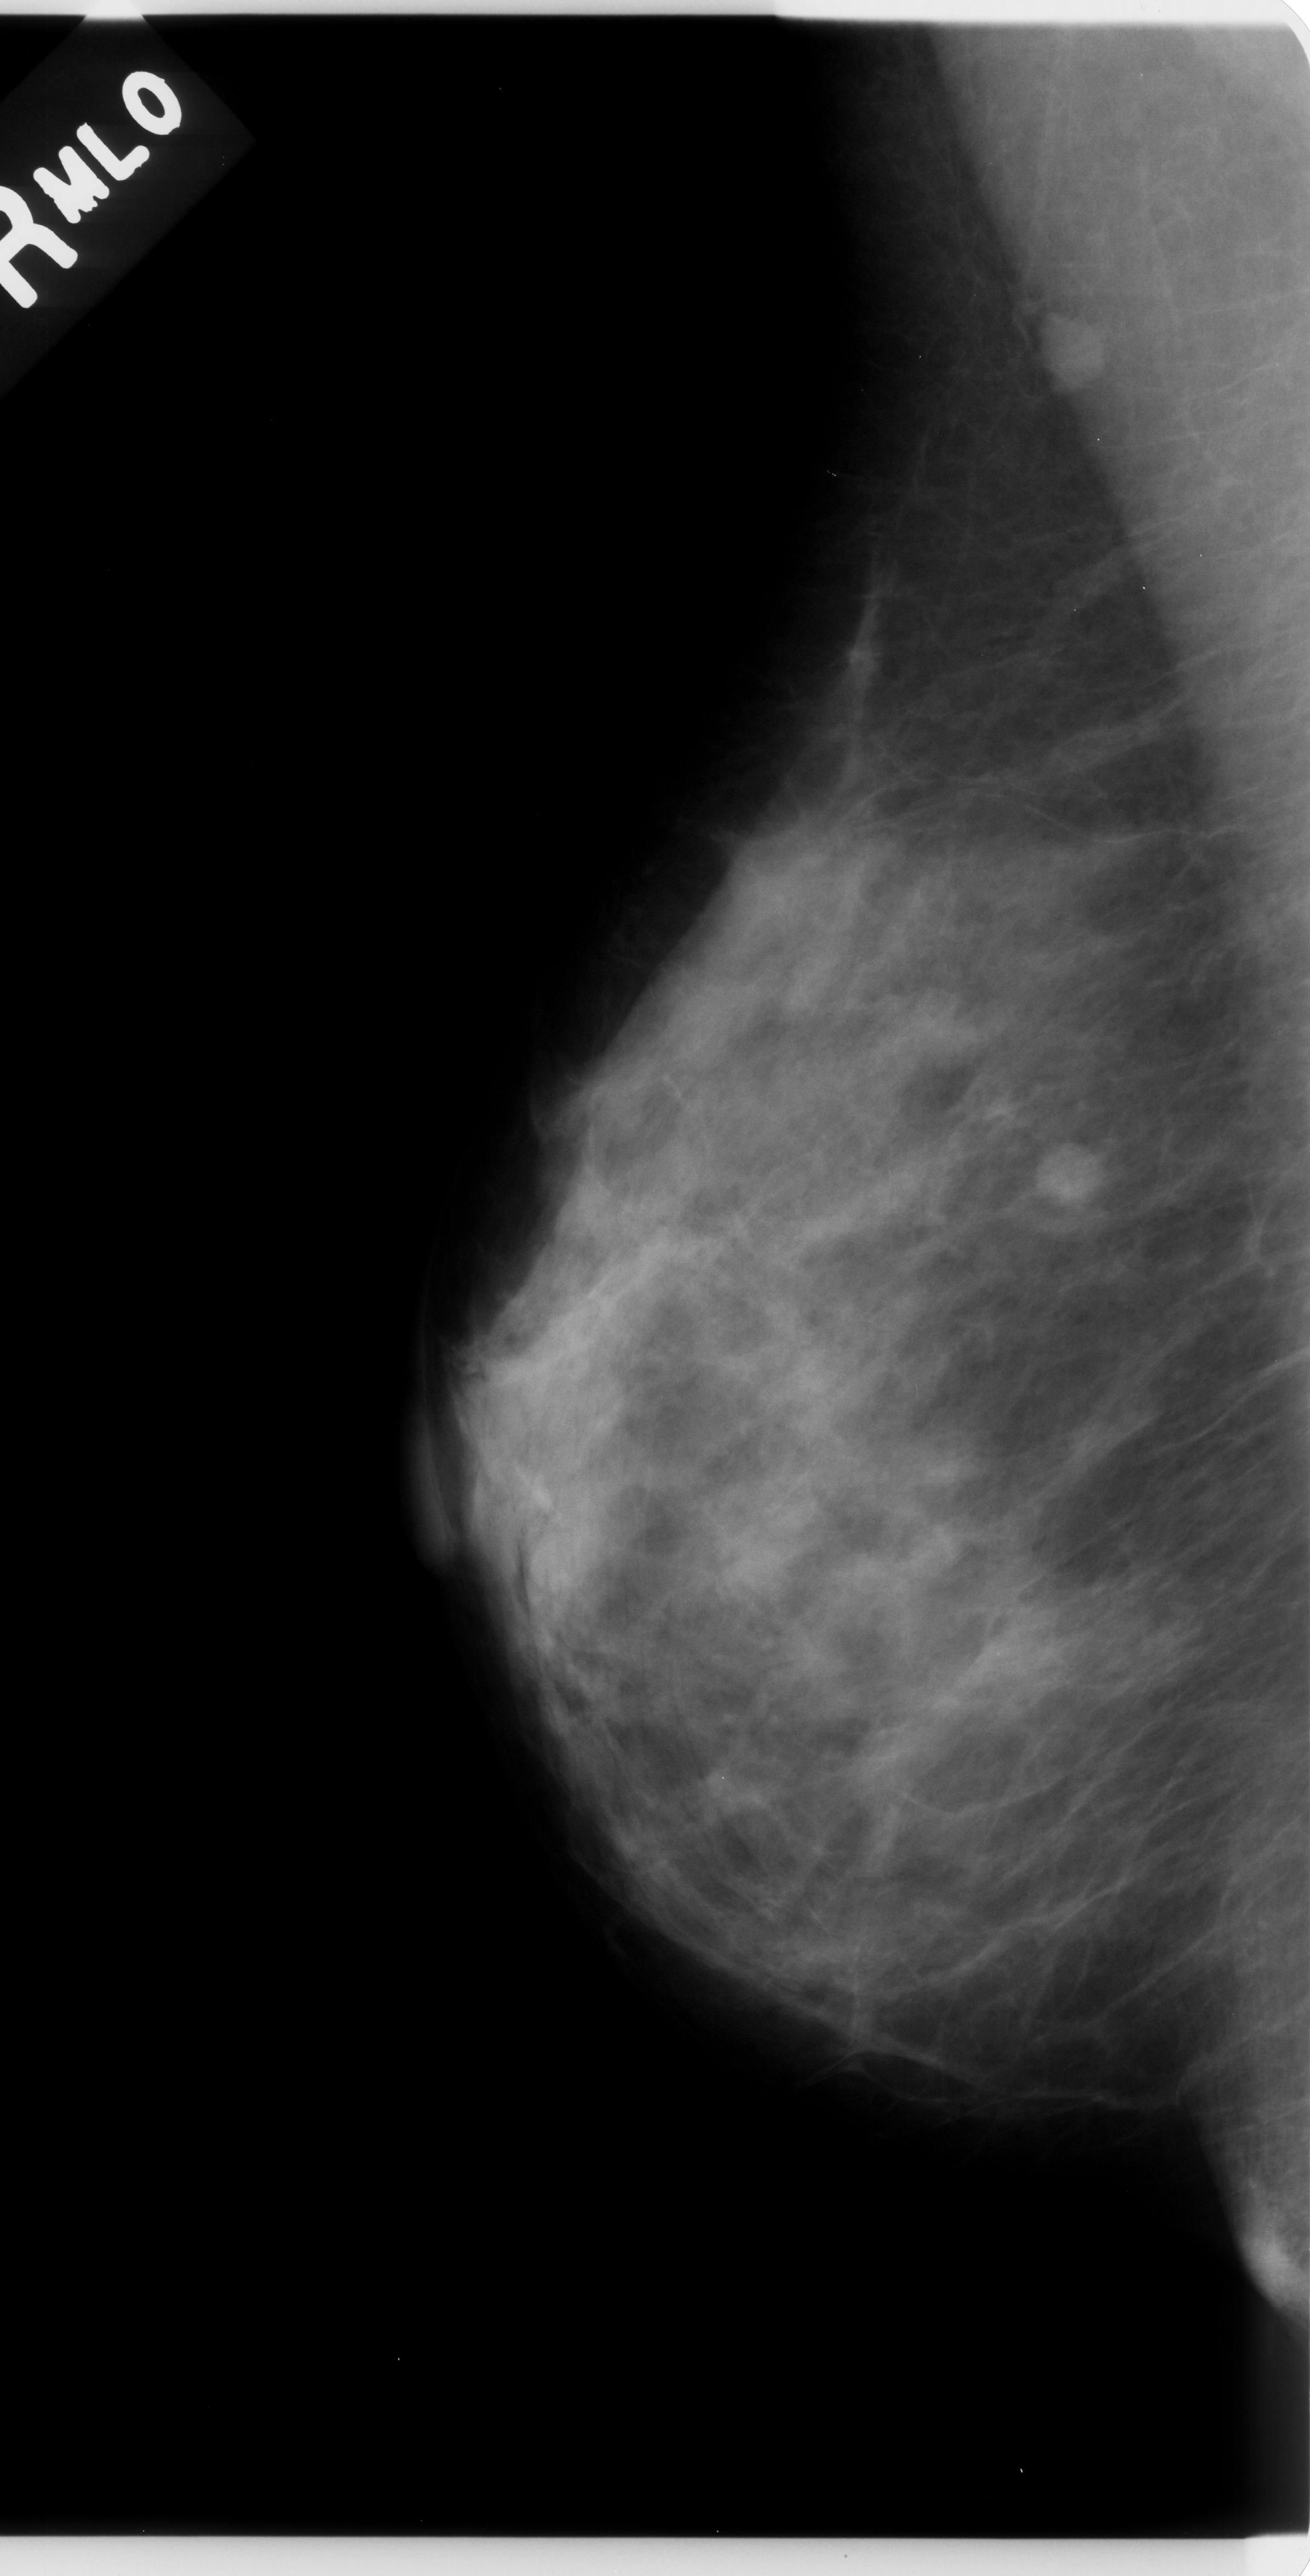
Mammogram (digitized film); right breast; mediolateral oblique (MLO) view; breast composition: scattered fibroglandular densities (BI-RADS density category 2 of 4).
Radiologist-marked abnormalities on this image: Finding 1 of 2: mass, shape round, margins circumscribed; BI-RADS assessment category 4; subtlety rating 5 on a 1 (subtle) to 5 (obvious) scale; pathology result (as recorded, not read from the image): malignant. Finding 2 of 2: mass, shape round, margins circumscribed; BI-RADS assessment category 4; subtlety rating 5 on a 1 (subtle) to 5 (obvious) scale; pathology (as recorded): malignant.